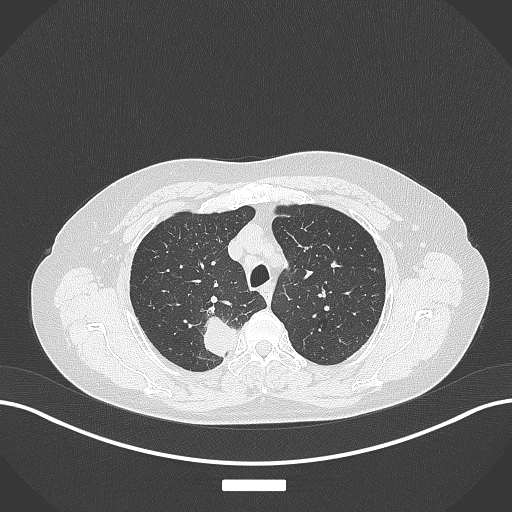
Chest CT, one axial slice. Slice 306 of 357 in the series (ordered by position). Reconstruction kernel B70f. Lung window (W 1500 / L -600 HU). 512 × 512 image matrix, field of view 400 × 400 mm. Female patient, age 62 years. From the clinical record (not read from this slice): clinical TNM (as recorded): T1c N1 M0.
Structures marked on this image (bounding box drawn by a radiologist):
- lung tumour (recorded histology: squamous cell carcinoma): bounding box [x1, y1, x2, y2] px = [198, 307, 234, 360]